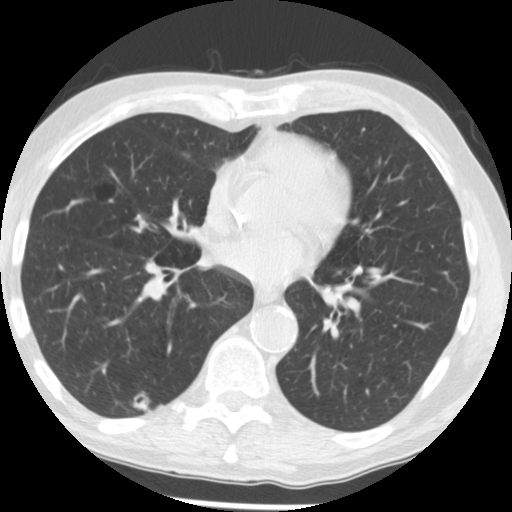
Low-dose screening chest CT, axial slice. Second screening round (one year after baseline). Lung window (W 1500 / L -600 HU). Male participant, aged 62 years at enrolment. Current smoker at enrolment.
Expert-annotated lung lesion, box from (x=125, y=386) to (x=162, y=420) px. The screening reader recorded 2 non-calcified nodules or masses ≥4 mm on this exam (right lower lobe, right lower lobe); which of them this box marks is not recorded. Later outcome: lung cancer diagnosed 506 days after this screen (after the third annual screen) — adenocarcinoma, NOS, right lower lobe, moderately differentiated (G2), stage IIIB (AJCC 6th edition), 15 mm at pathology.